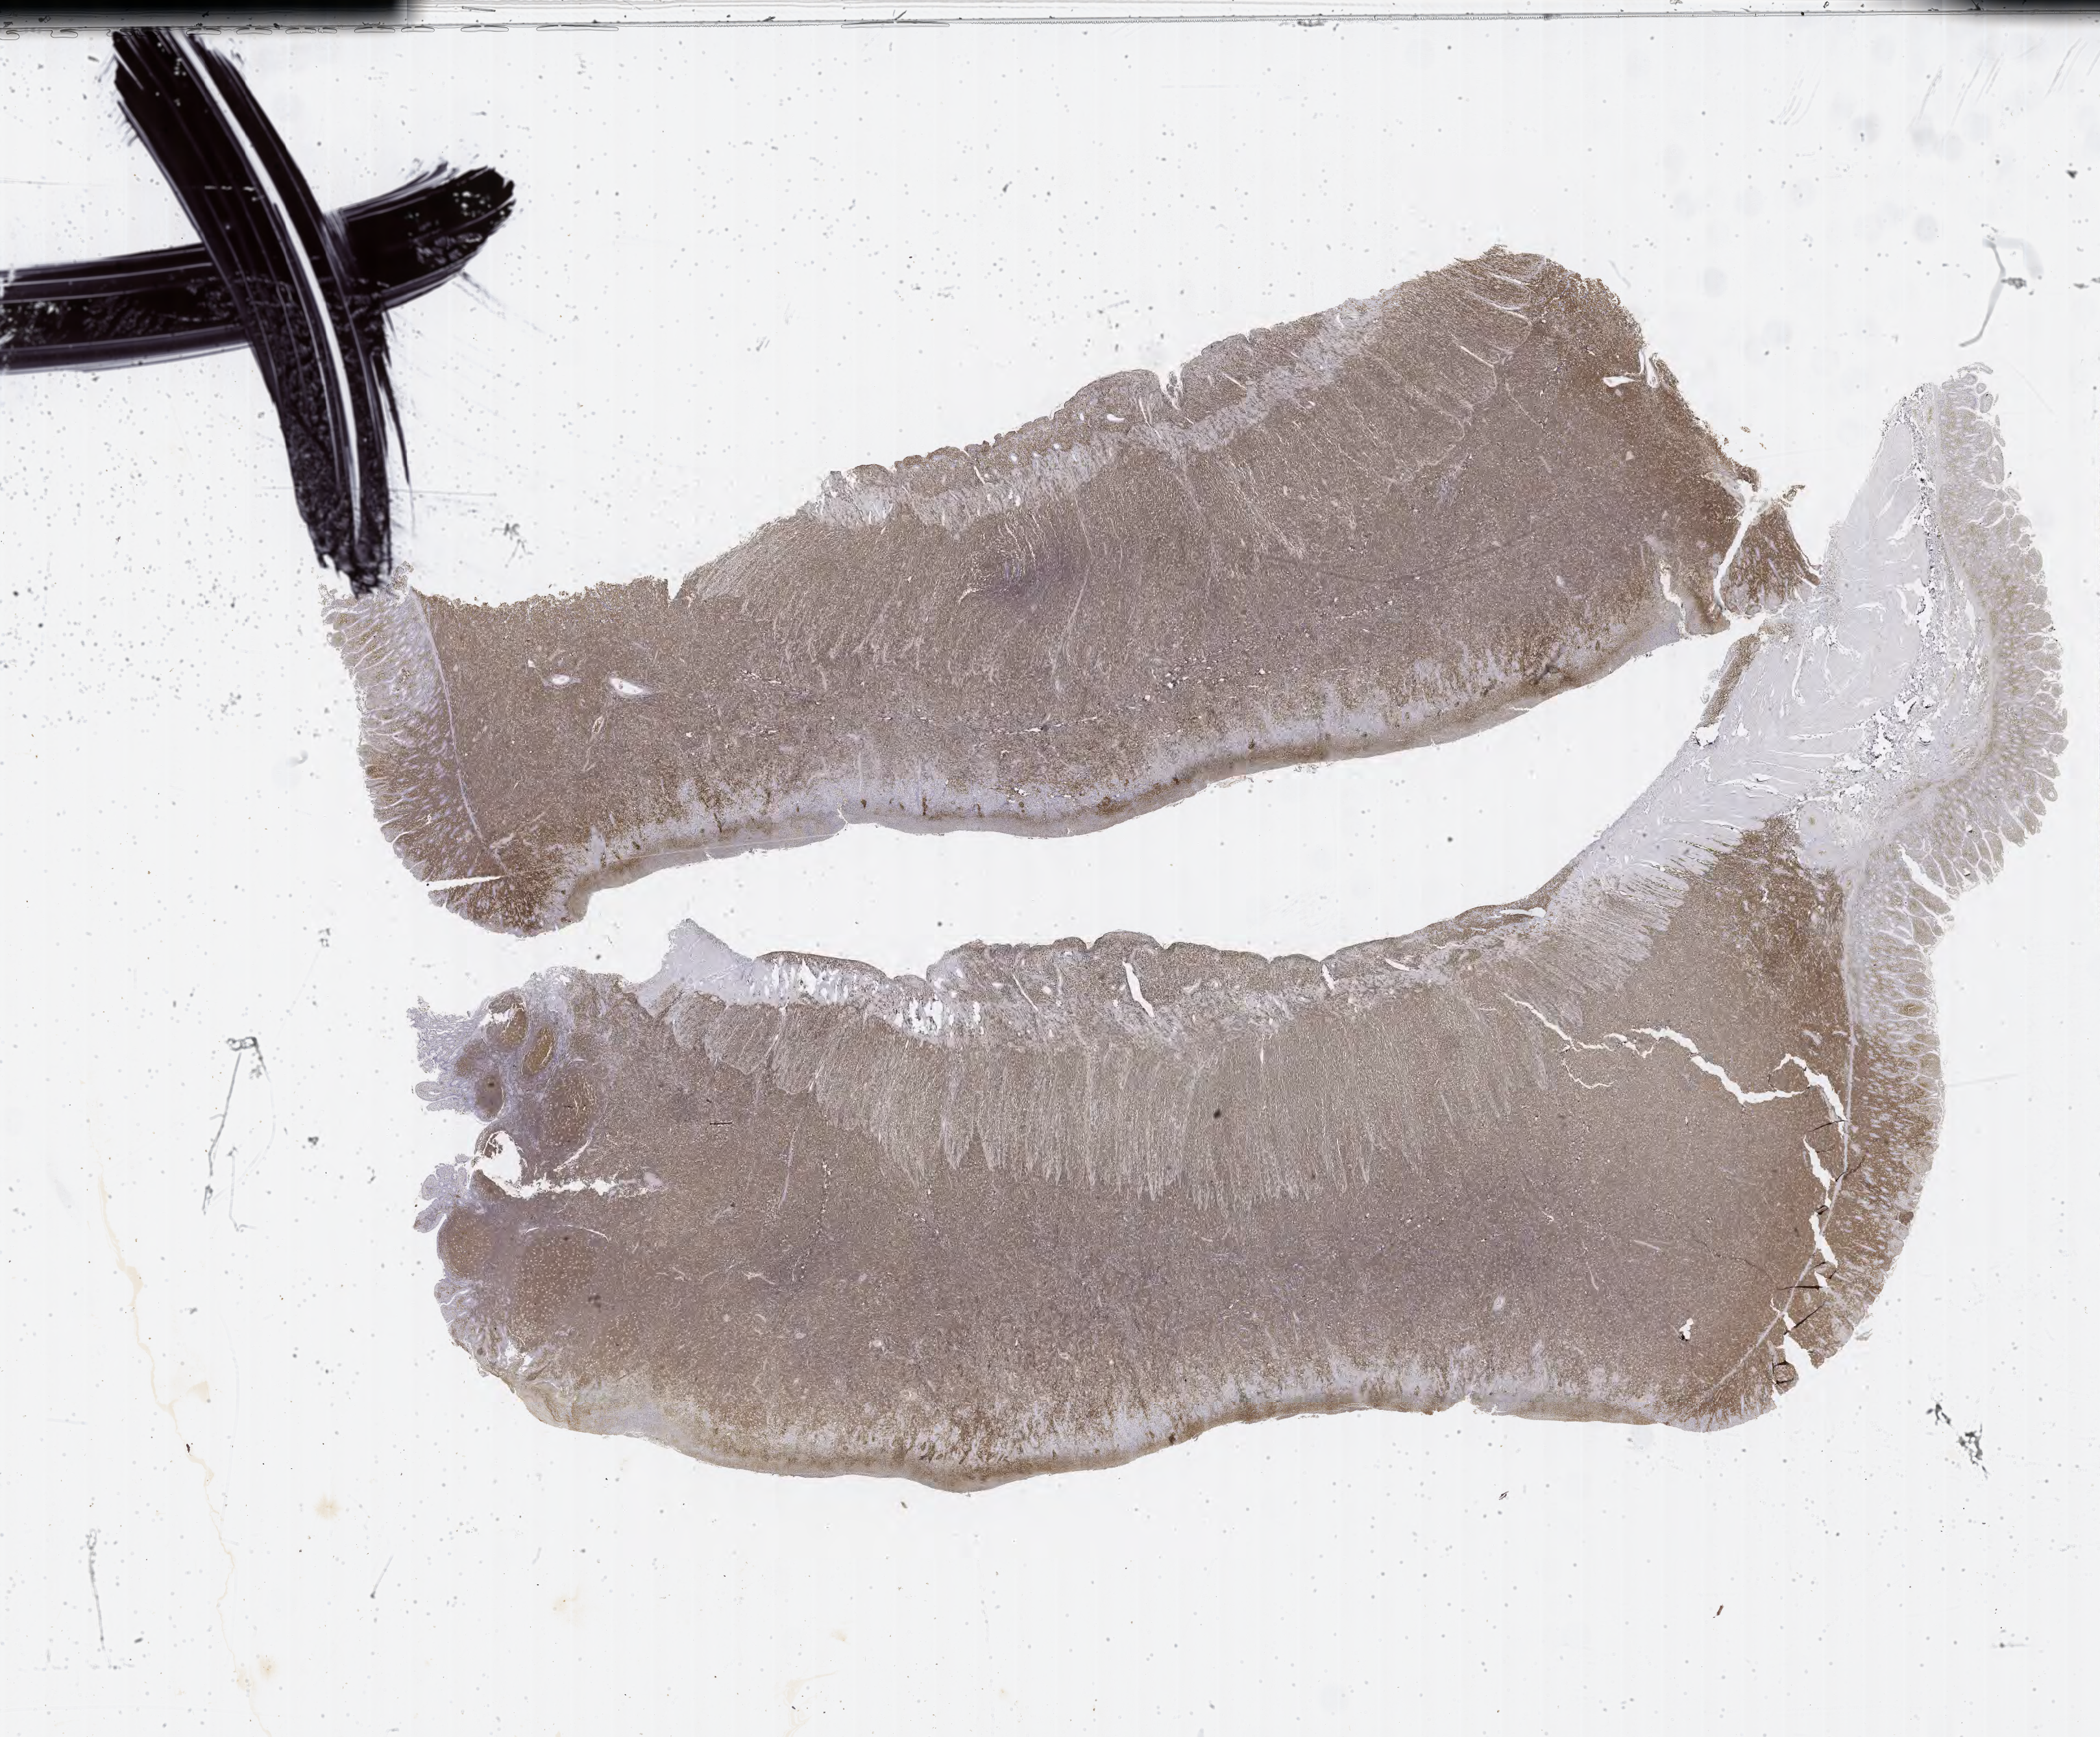
IHC for CD20, whole-slide image, a low-resolution overview of the entire scanned area, about 26.2 x 21.6 mm; specimen: tumor tissue. Female patient, age 27 years.
* diagnosis: Burkitt lymphoma, NOS